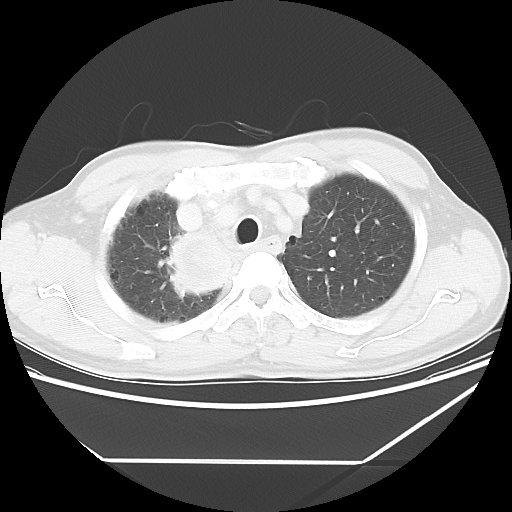
Chest CT, one axial slice. Slice 49 of 60 in the series (ordered by position). Reconstruction kernel LUNG. Lung window (W 1500 / L -600 HU). 5 mm slice thickness. 512 × 512 image matrix, field of view 367 × 367 mm. Male patient, age 58 years. Case-level facts recorded for this patient, not image findings: clinical TNM (as recorded): T2 N2 M0.
Structures marked on this image (bounding box drawn by a radiologist):
- lung tumour (recorded histology: squamous cell carcinoma): bounding box [x1, y1, x2, y2] px = [154, 213, 232, 306]